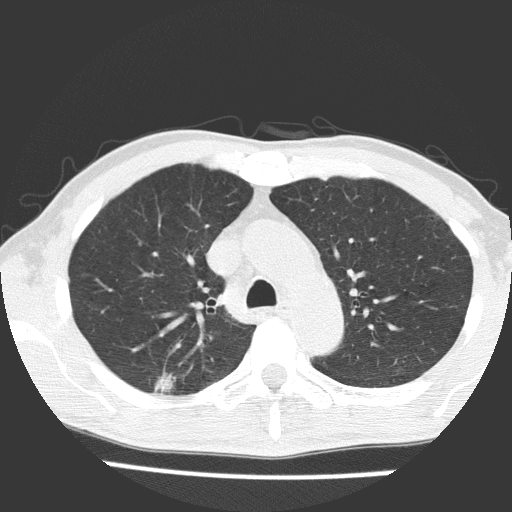
Low-dose screening chest CT, one axial slice. Slice 115 of 160 in the series (ordered by position). Reconstruction kernel FC51. 120 kVp. Lung window (W 1500 / L -600 HU). 2 mm slice thickness. 512 × 512 image matrix.
Annotated regions visible in this slice (manually delineated by an expert):
- lesion 1 (tumor, upper lobe of right lung): bounding box [x1, y1, x2, y2] px = [154, 373, 176, 394]